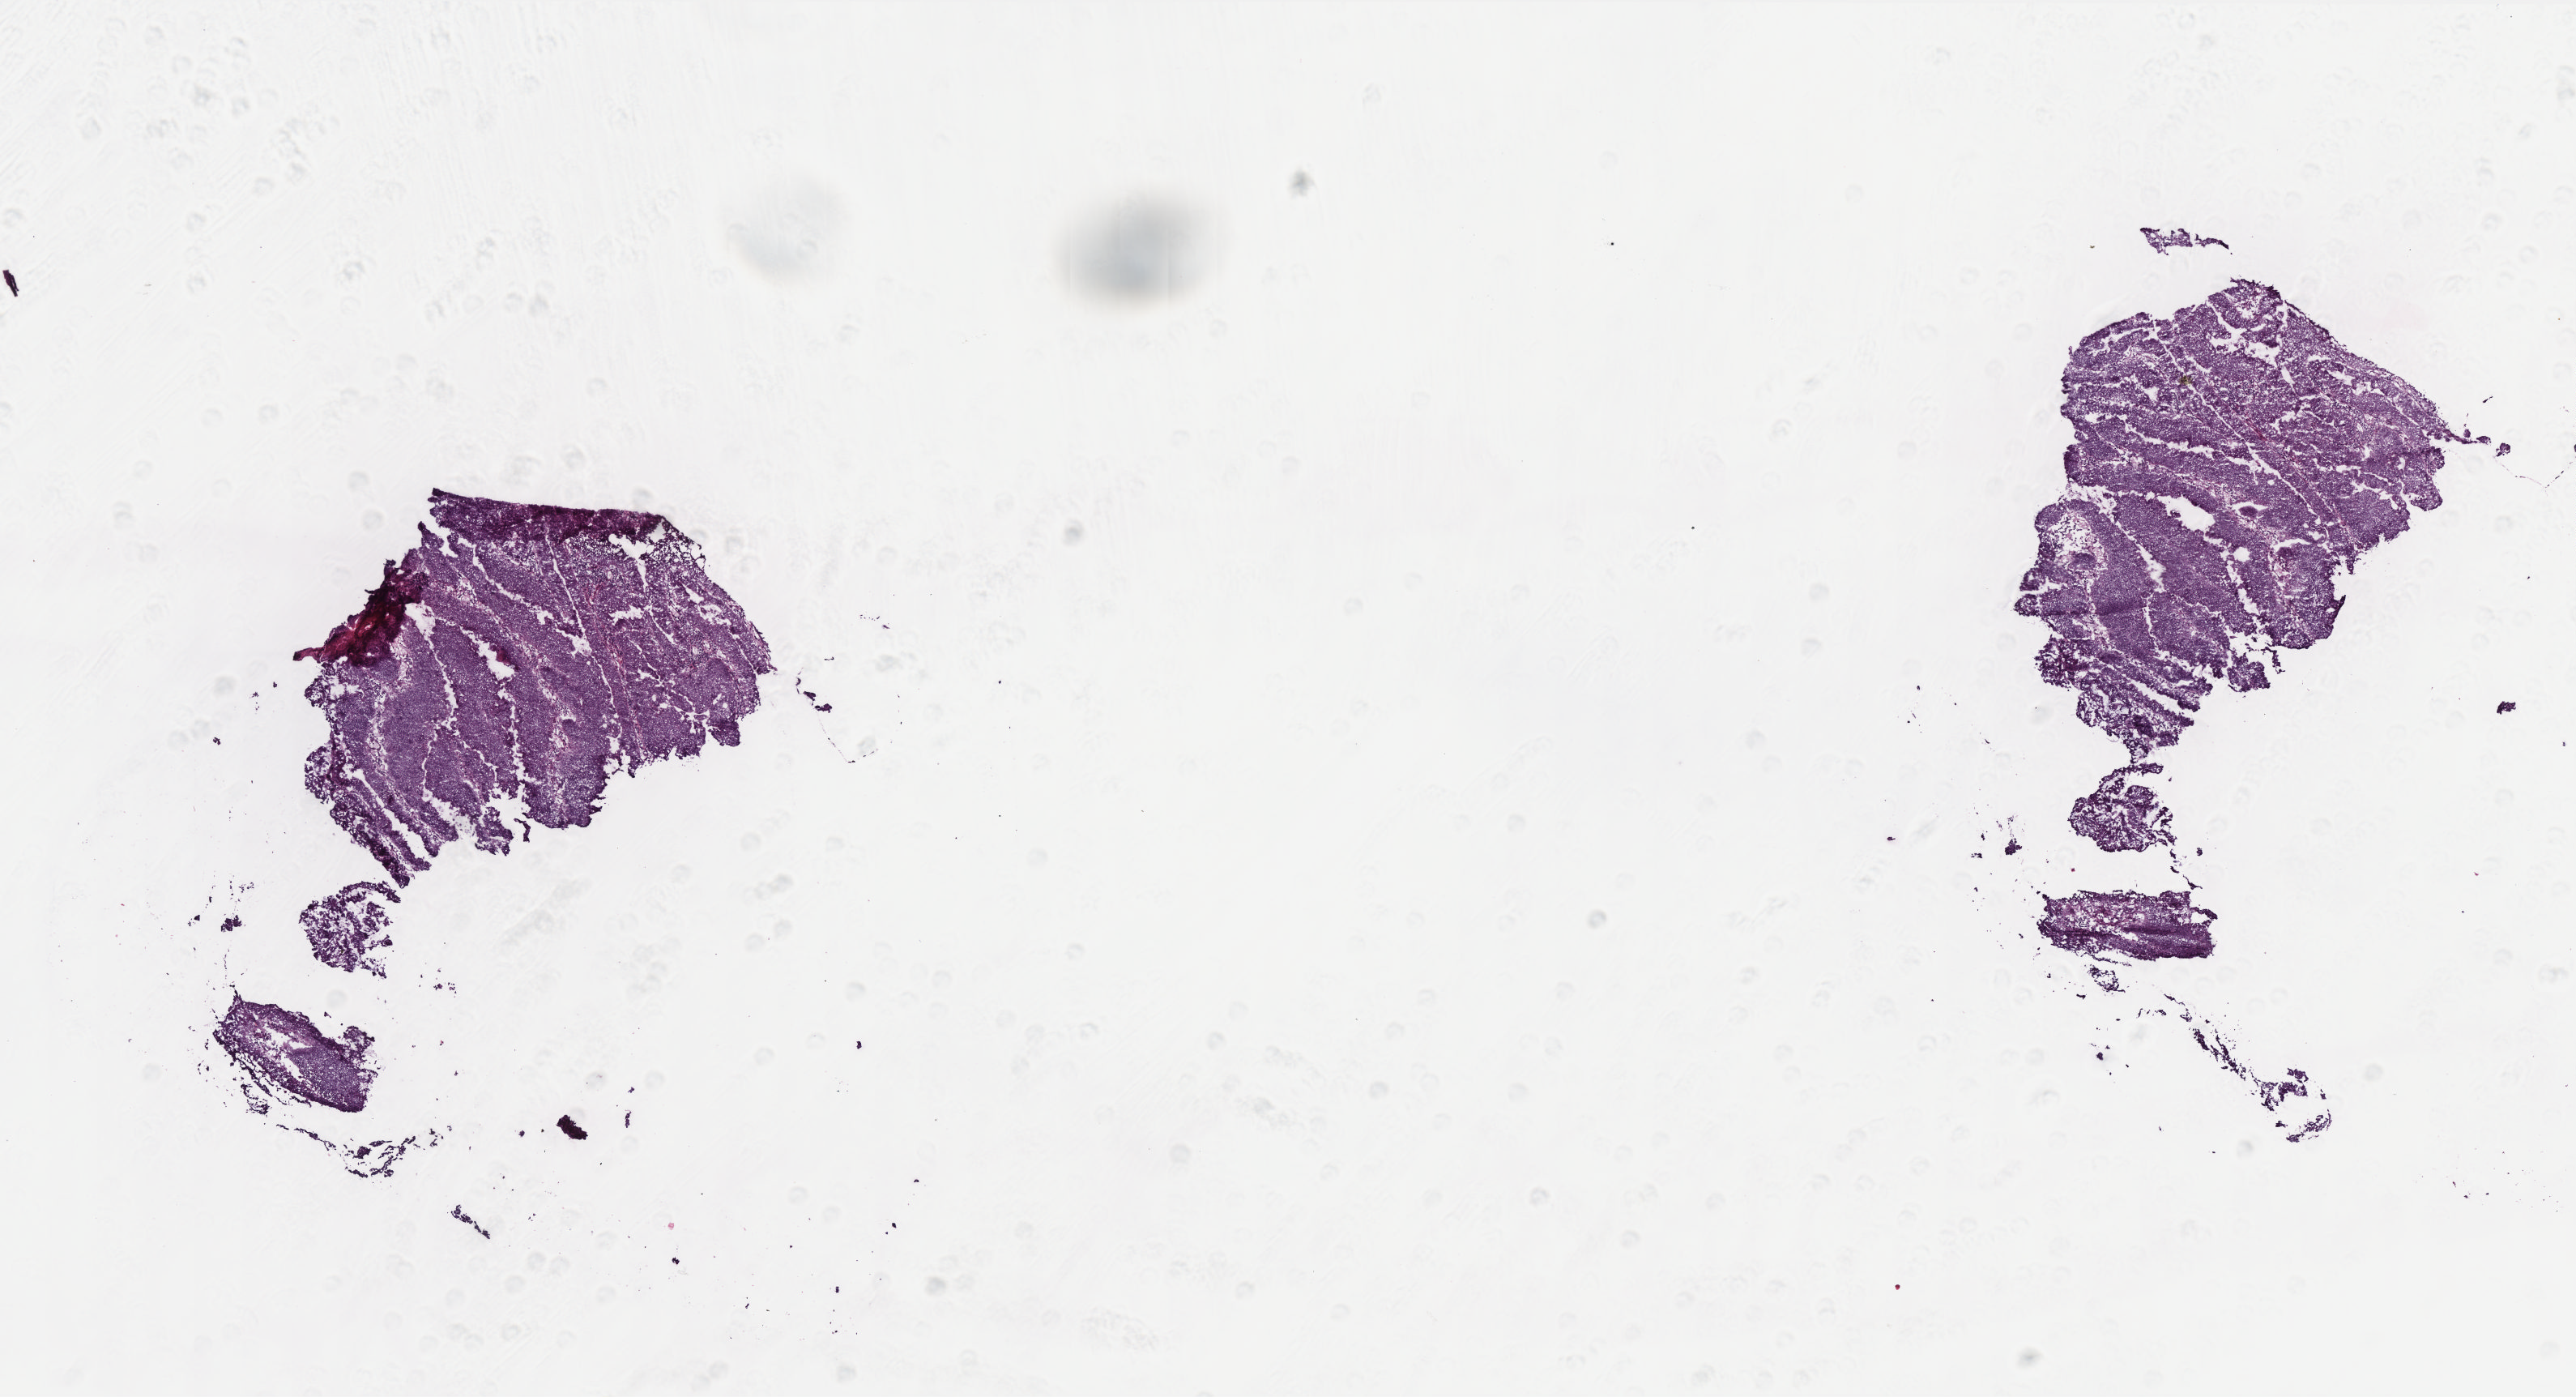
Digitized H&E-stained tissue section (whole slide), low-resolution overview of the scanned area, about 12.7 x 6.9 mm, frozen section, sample: primary tumour, colon. Patient: male, age at initial diagnosis 80 years. Composition of this section per pathologist review: tumour cells 95%, tumour nuclei 90%, normal cells 0%, stromal cells 4%, necrosis 1%. Infiltration values recorded for this section: lymphocyte infiltration 3%, monocyte infiltration 1%, neutrophil infiltration 1%.
- pathologic diagnosis: Adenocarcinoma, NOS (sigmoid colon)
- lymph nodes positive (case pathology): 0 of 17 examined
- AJCC pathologic stage: I